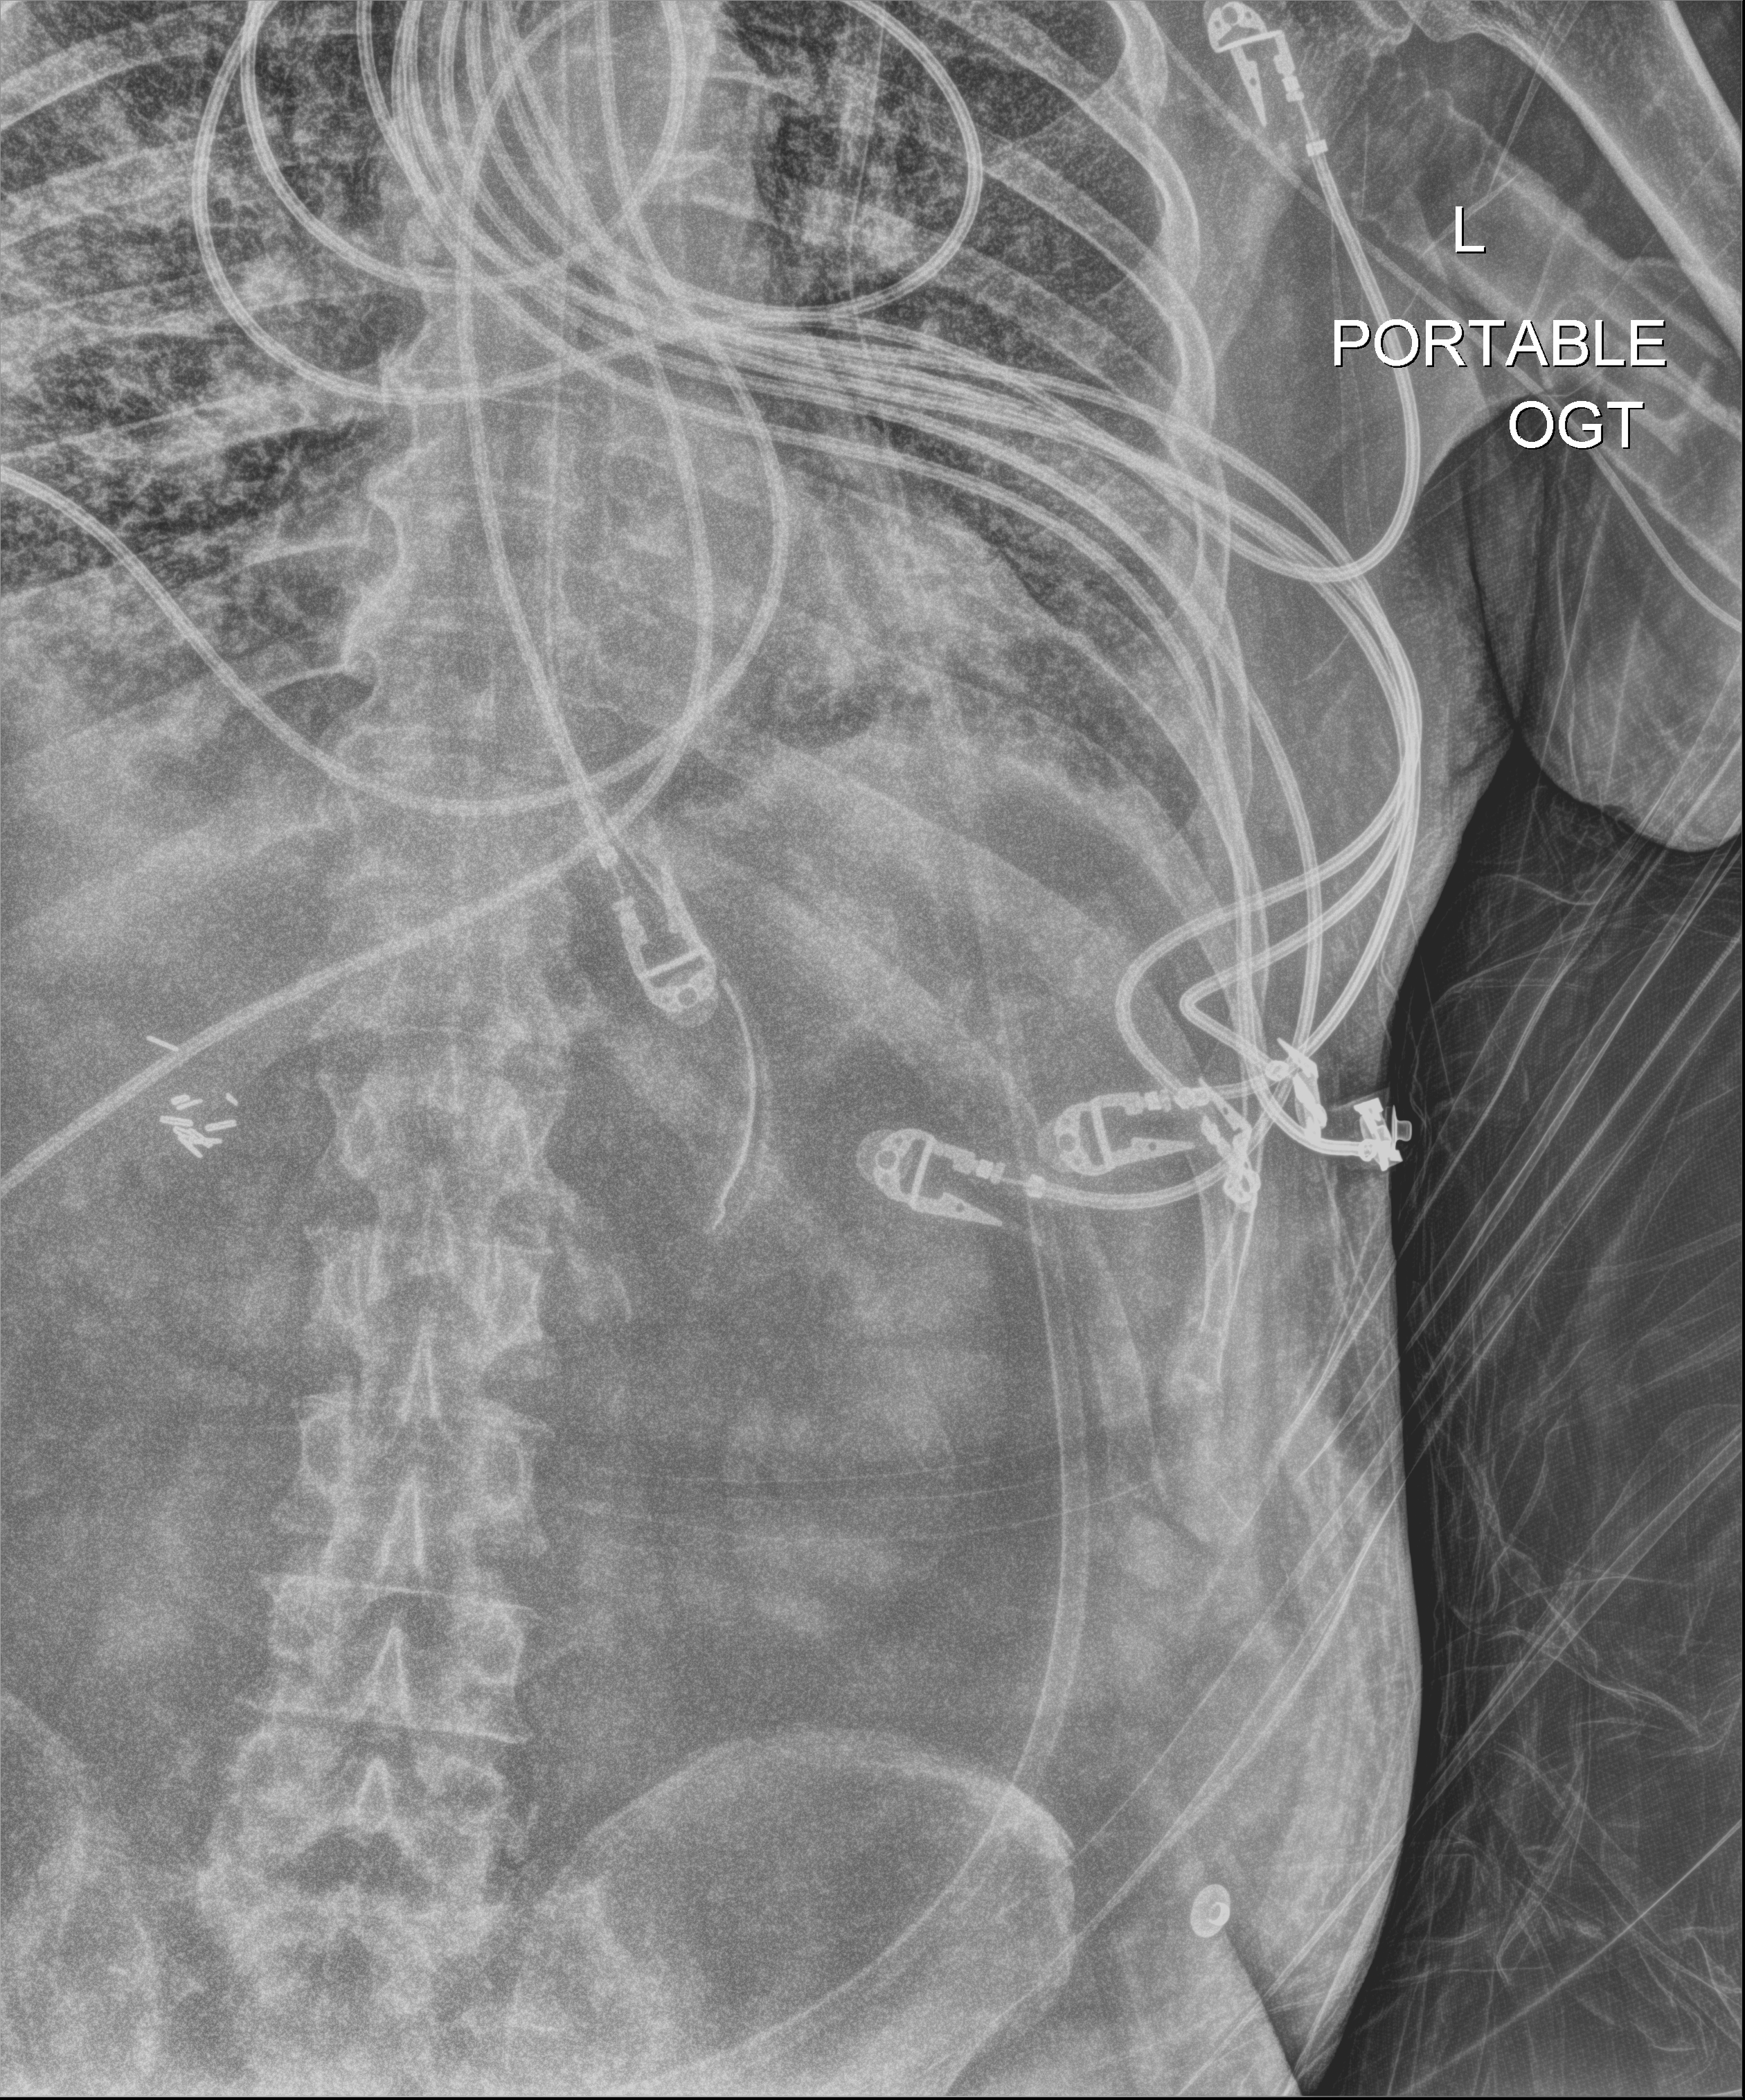
Chest X-ray; anteroposterior (AP) projection. Male patient hospitalised with COVID-19, age 75–90 years.
Admission-level facts for this patient (not findings on this image; timing relative to this image not recorded):
- admitted to intensive care during this hospital stay: yes
- mechanically ventilated during this hospital stay: yes
- COPD (admission record): no